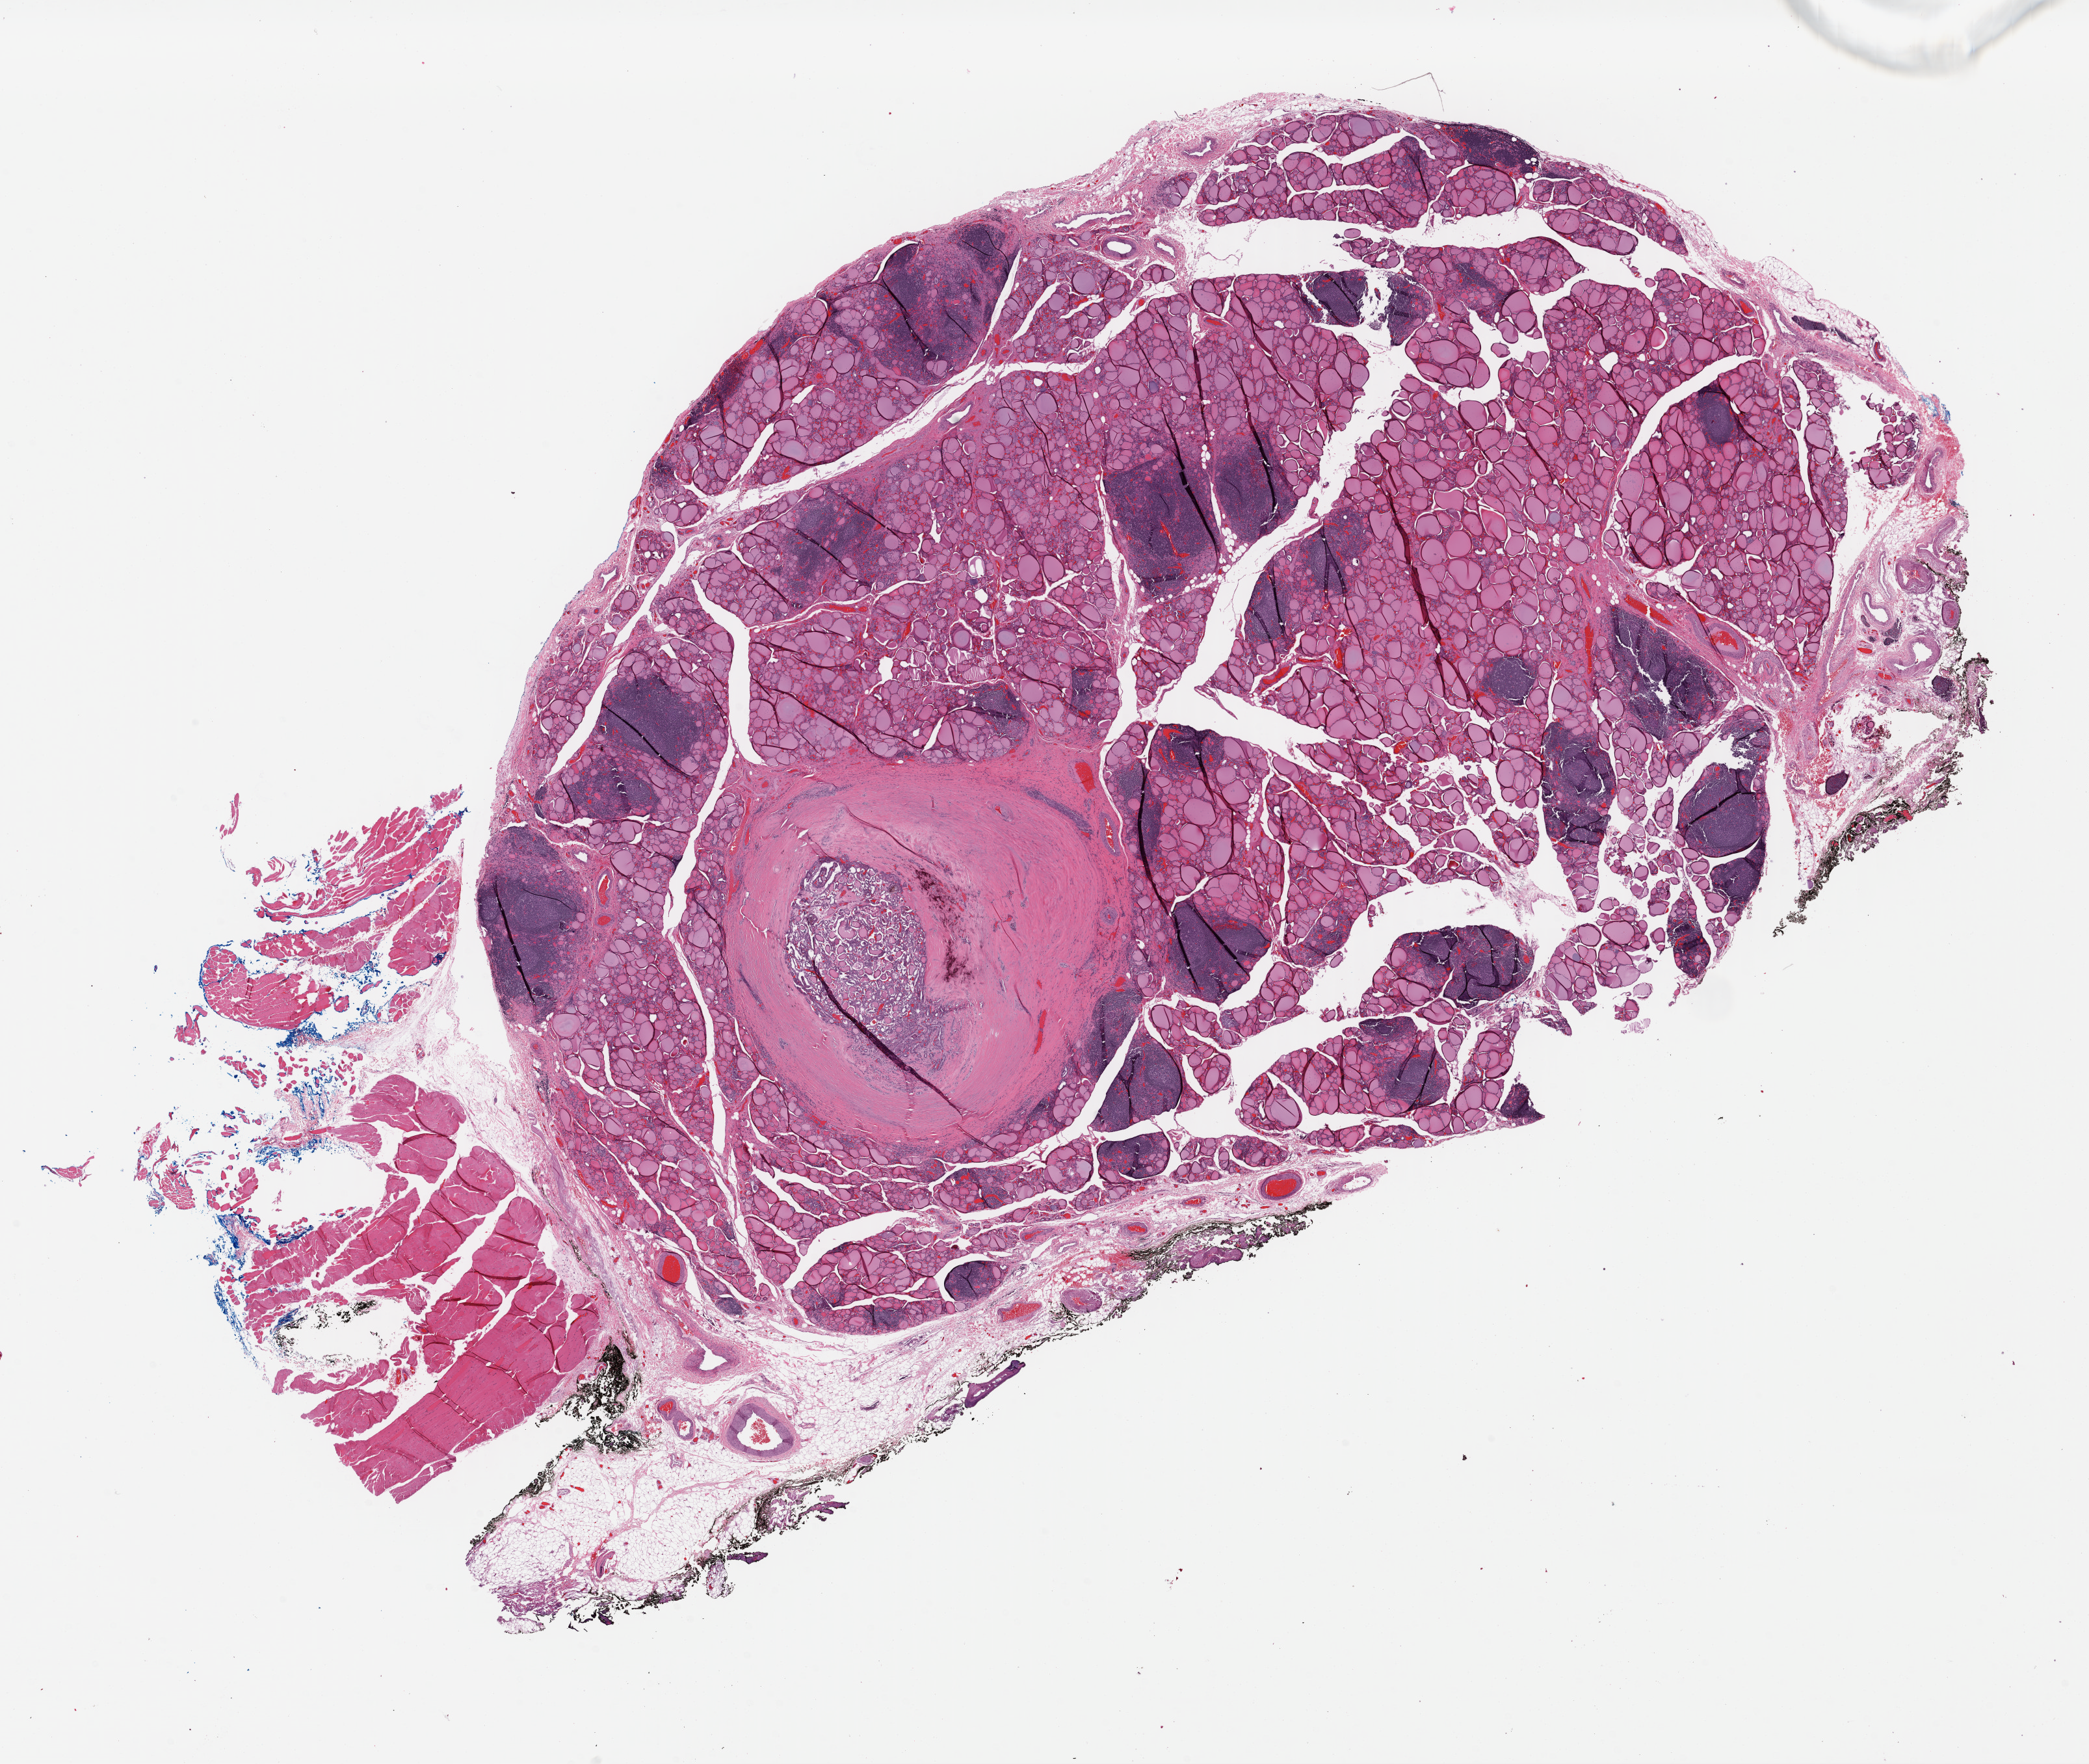
Digitized H&E tissue section (whole slide) — whole scanned area (about 25.3 x 21.3 mm, slide scanned at 40x) shown as a low-resolution overview; formalin-fixed paraffin-embedded (FFPE) diagnostic section; thyroid, primary tumour sample. Male patient; age at initial diagnosis 54 years.
* pathologic diagnosis: Papillary adenocarcinoma, NOS (thyroid gland)
* laterality: bilateral
* lymph nodes positive (case pathology): 0 of 4 examined
* AJCC pathologic stage: I (7th edition)